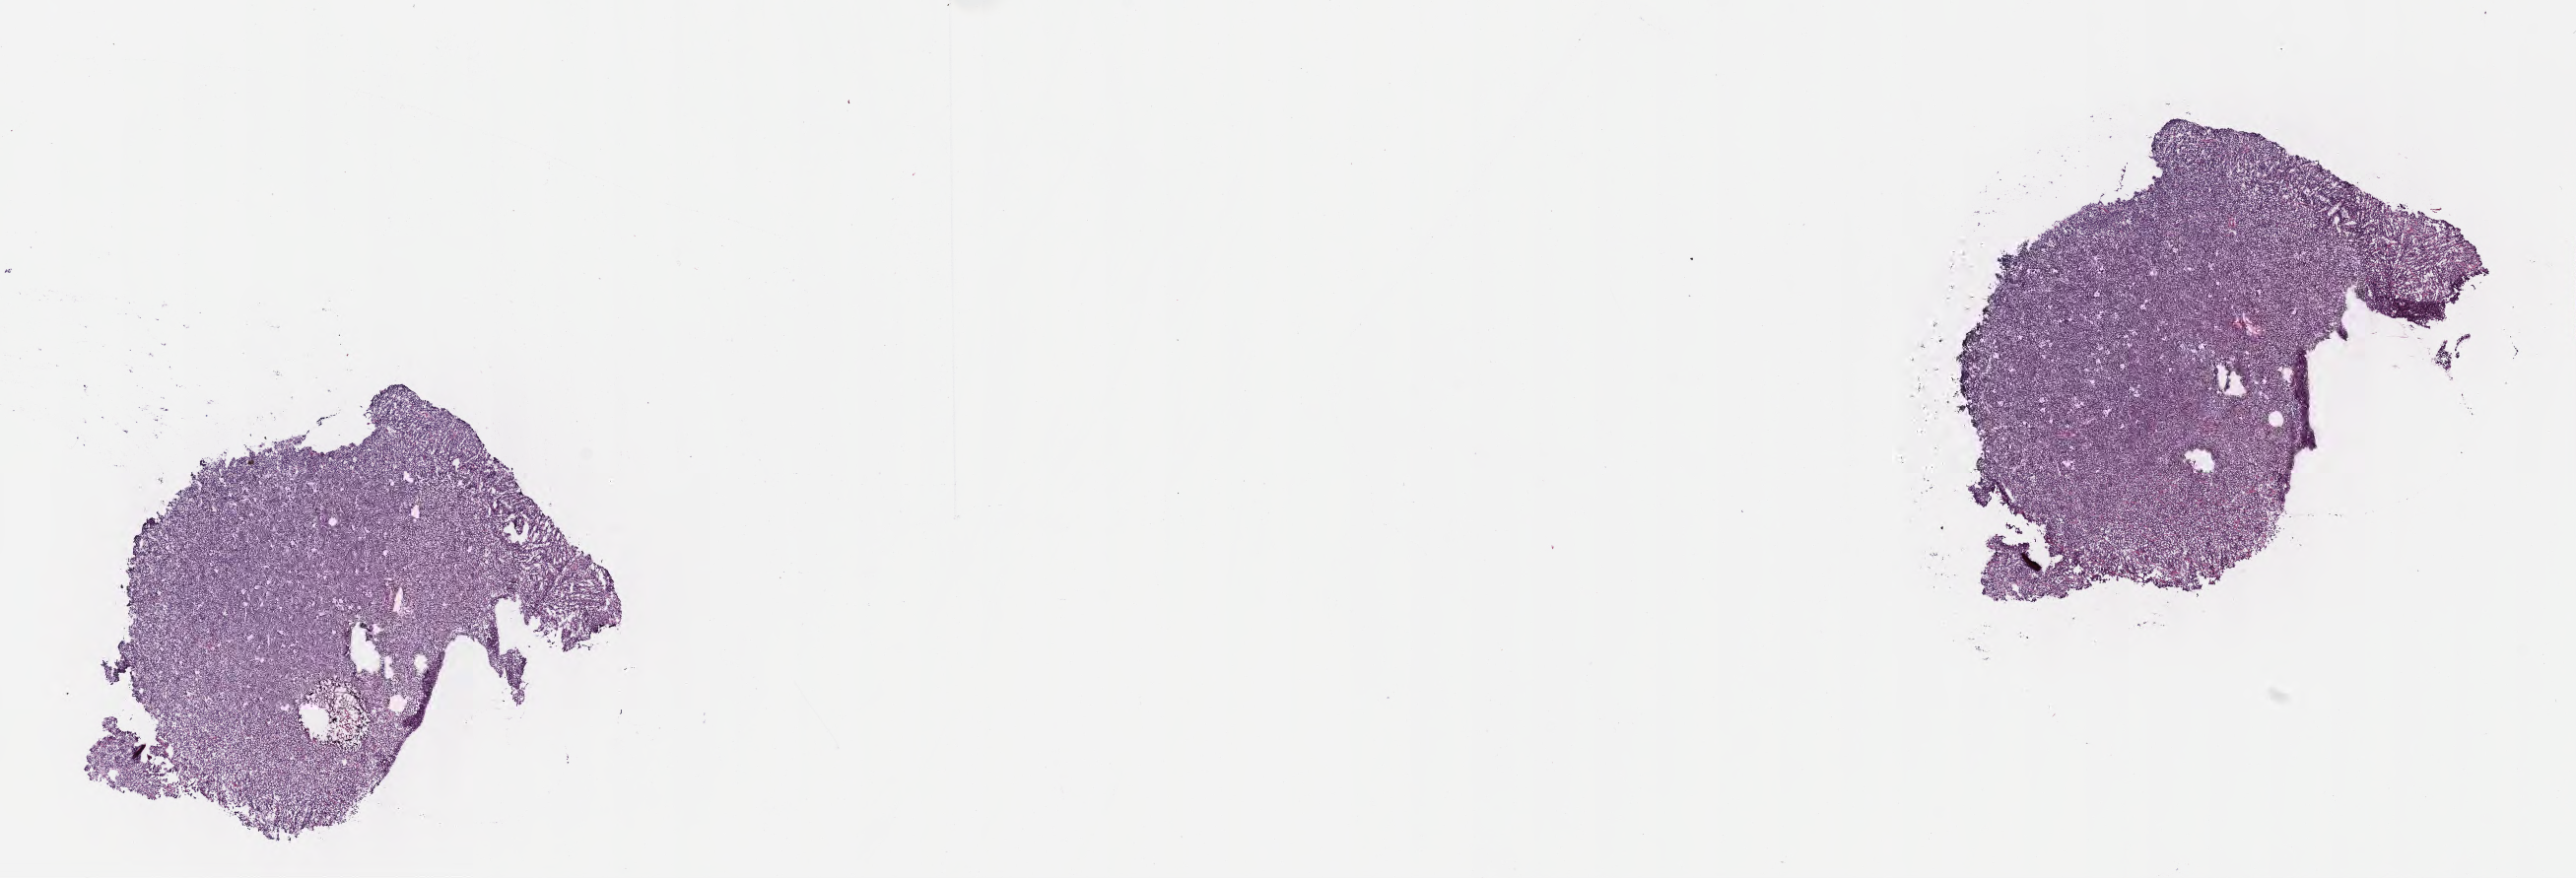
Whole-slide image, haematoxylin and eosin stain — shown as a low-resolution overview of the whole scanned area (about 21.1 x 7.2 mm); frozen section; specimen: primary tumor; anatomic site: cranium. Male patient; age at initial diagnosis 5 years.
Diagnosis: Burkitt lymphoma, NOS.